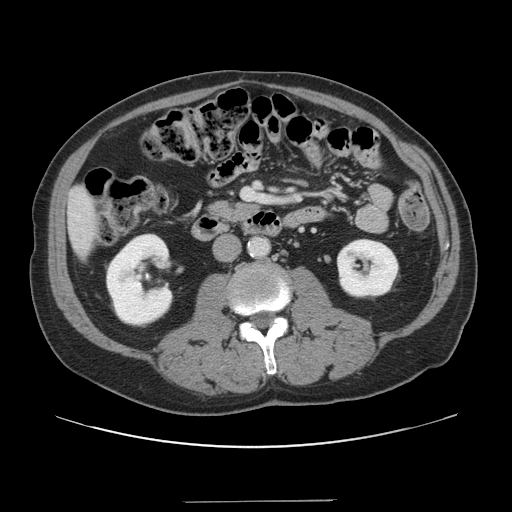
Contrast-enhanced abdominal CT, one axial slice; position 41 of 151 along the scan axis; intravenous contrast given; soft-tissue window (W 400 / L 40 HU); 2.5 mm slice thickness; 512 × 512 image matrix, field of view 399 × 399 mm. Male patient, age 63 years. From the clinical record (not read from this slice): diagnosis: colorectal cancer liver metastases, imaged before liver resection; multiple liver metastases: no; largest metastasis: 2.1 cm; disease in both lobes: no.
Structures marked on this image (expert manual segmentation):
- liver: bounding box [x1, y1, x2, y2] px = [69, 187, 100, 255]
- planned liver remnant (the part of the liver to remain after resection): [69, 187, 99, 255]
- portal vein (with intrahepatic branches): [243, 189, 268, 202]